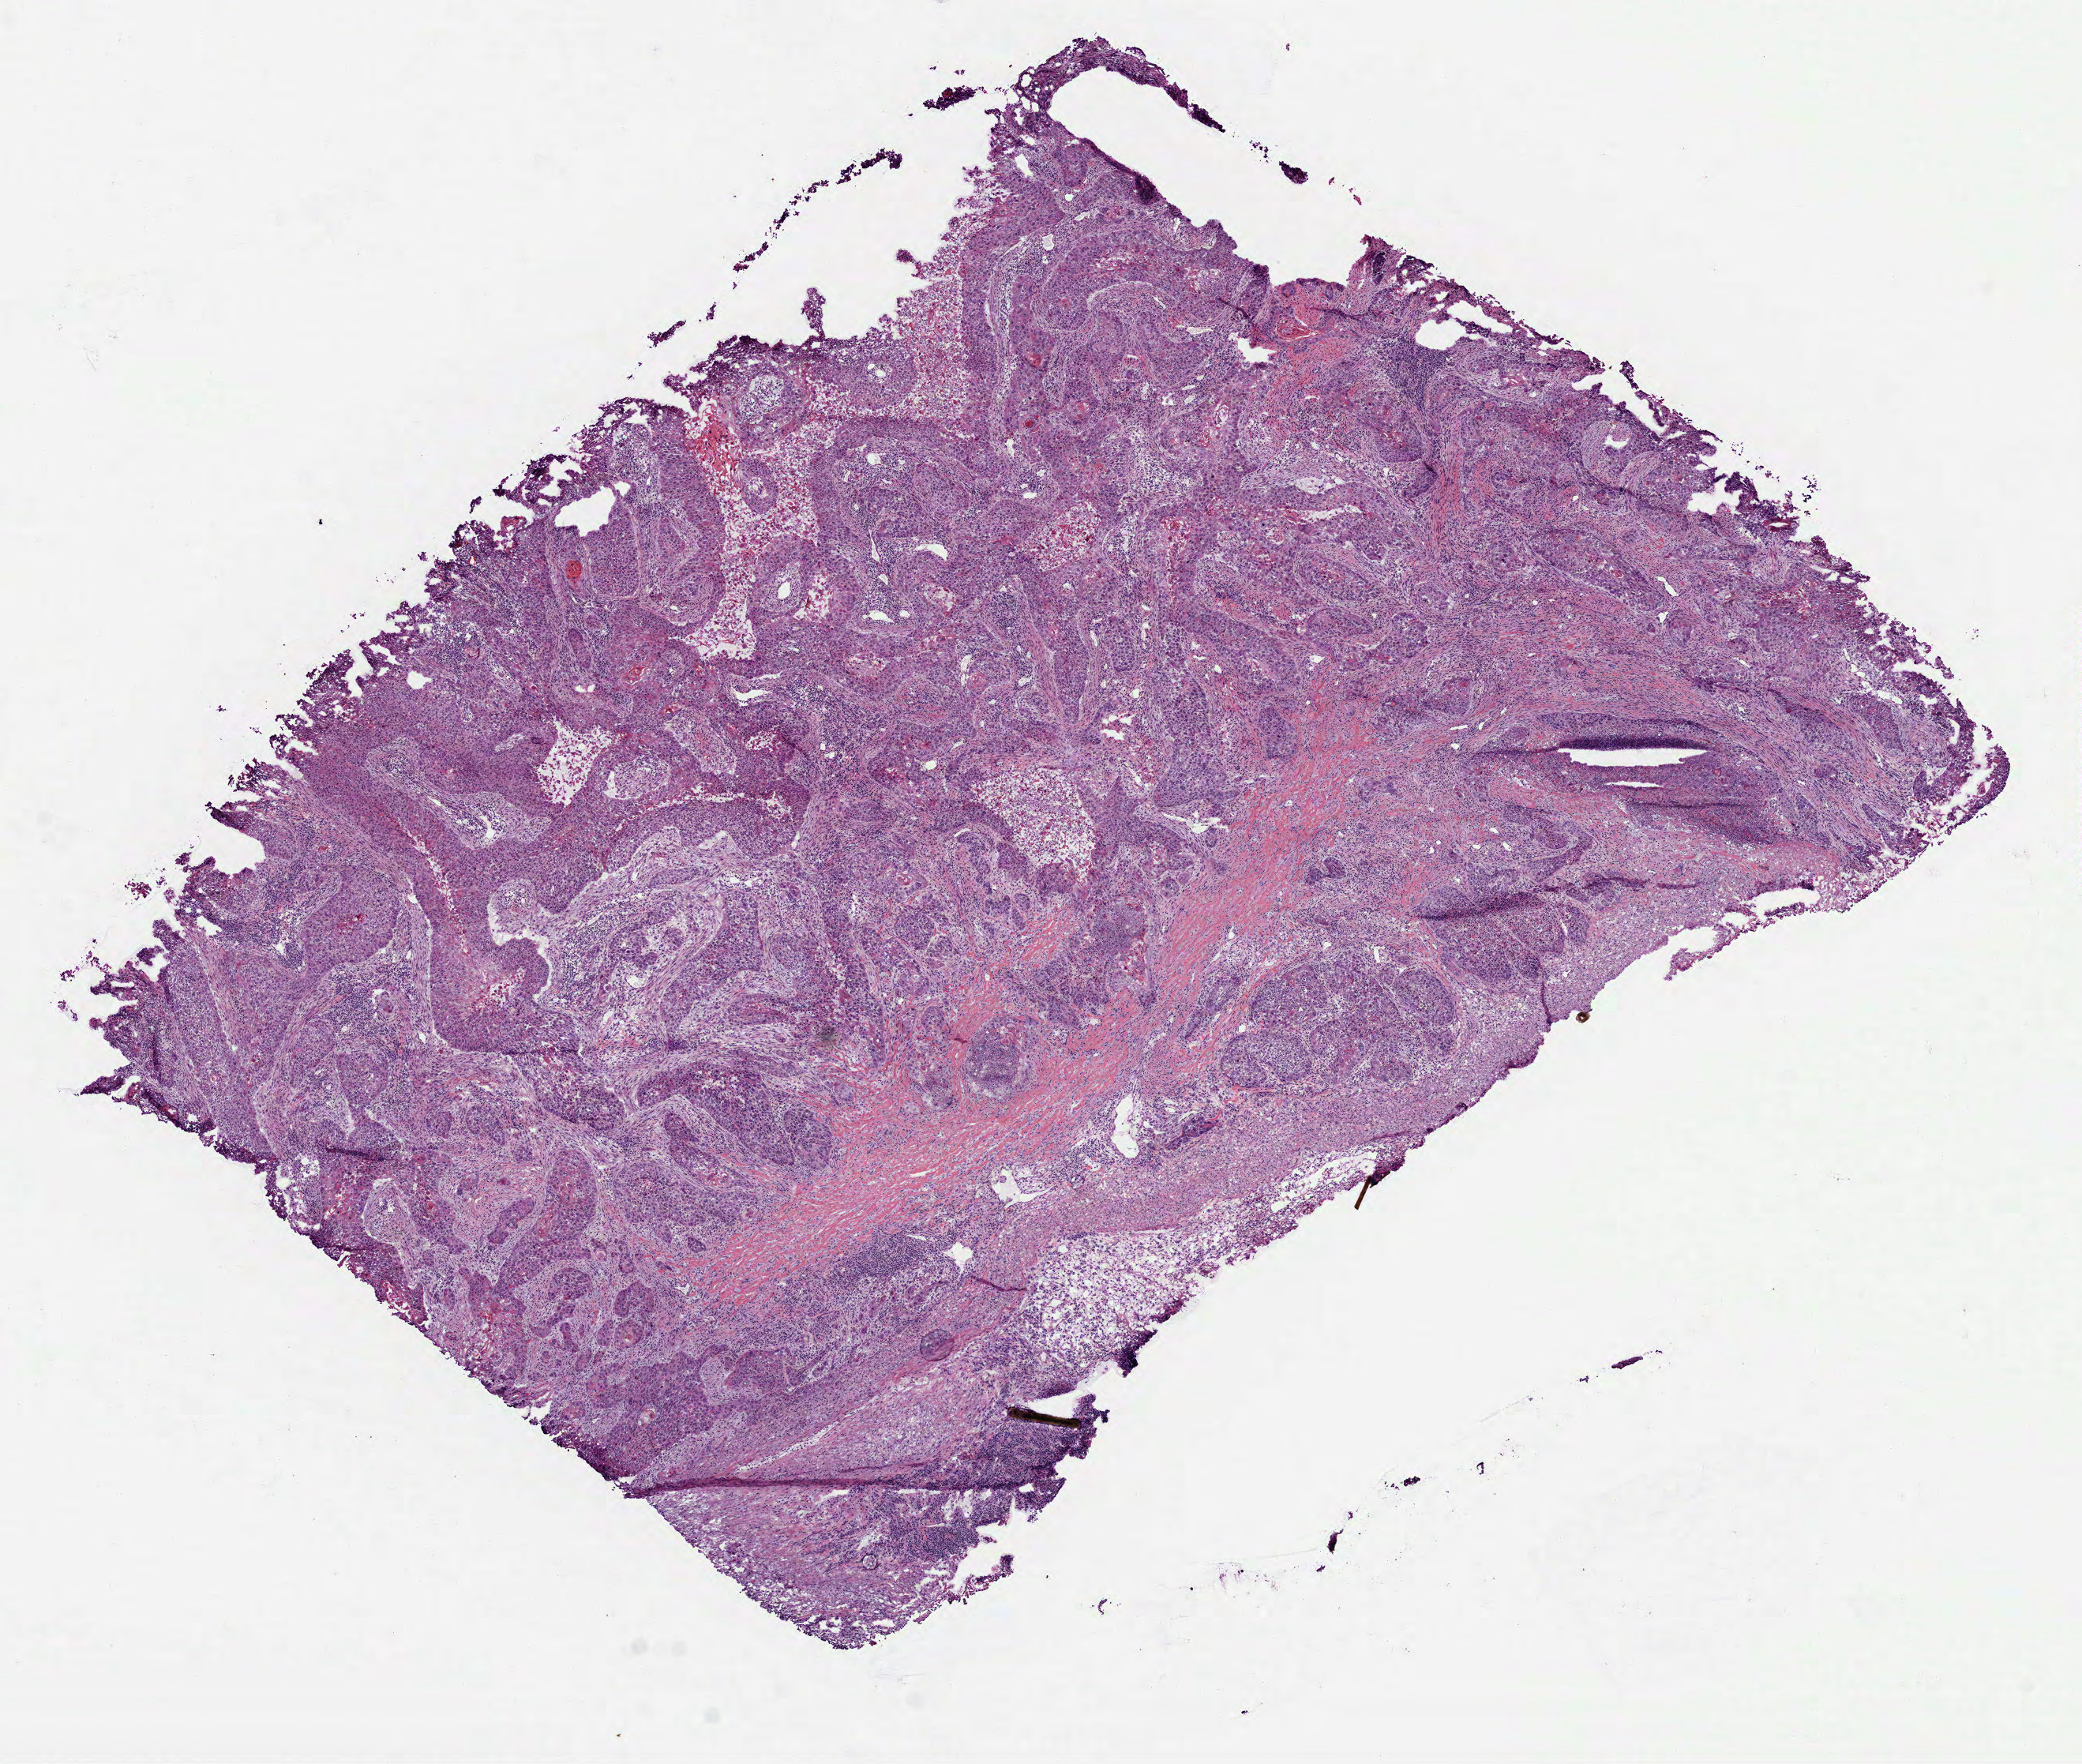
H&E-stained whole-slide image — low-resolution overview of the scanned area, about 10.6 x 9.0 mm (from a 40x scan); frozen section; primary tumour sample from the lung. Patient: male, age at initial diagnosis 65 years. Pathologist review of this section (percent, as recorded): tumour cells 100%, tumour nuclei 65%, normal cells 0%, stromal cells 0%, necrosis 0%. Inflammatory infiltration, as recorded: lymphocyte infiltration 15%, monocyte infiltration 0%, neutrophil infiltration 5%.
- diagnosis: Squamous cell carcinoma, NOS
- laterality: left
- AJCC pathologic stage: IIB